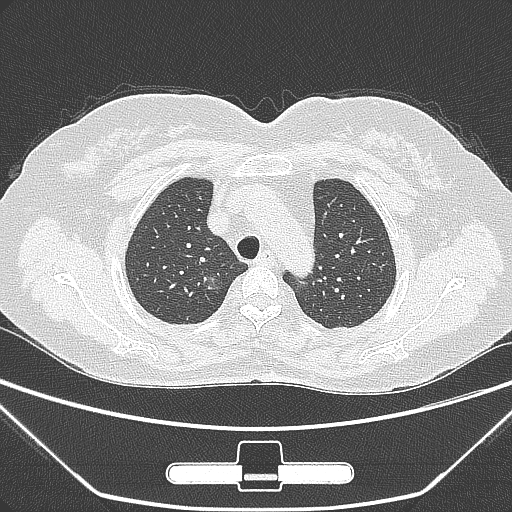
Chest CT, one axial slice. Position 224 of 275 along the scan axis. 120 kVp. Lung window (W 1500 / L -600 HU). 1 mm slice thickness. 512 × 512 image matrix, field of view 356 × 356 mm. Patient: female, 63 years. Case-level facts recorded for this patient, not image findings: clinical TNM (as recorded): T1a N0 M0; histopathological grade: G1.
Structures marked on this image (rectangle marked by the reading radiologist):
- lung tumour (recorded histology: adenocarcinoma): box from (x=196, y=268) to (x=219, y=297) px